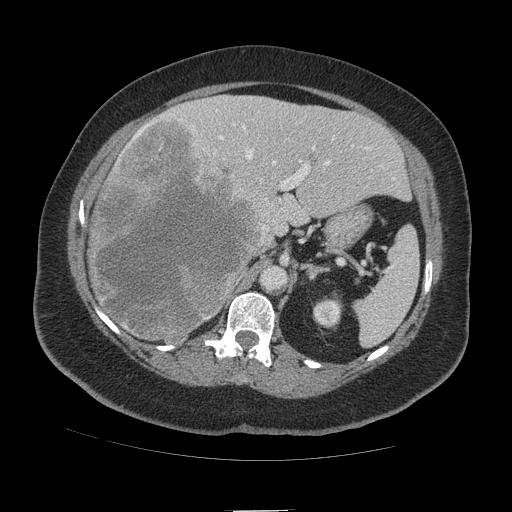
Contrast-enhanced abdominal CT (liver protocol), one axial slice; position 65 of 109 along the scan axis; soft-tissue window (W 400 / L 40 HU); 2.5 mm slice thickness; 512 × 512 image matrix. Case-level facts recorded for this patient, not image findings: diagnosis: hepatocellular carcinoma (patient treated with transarterial chemoembolisation; whether this scan precedes or follows treatment is not stated here); TNM stage (as recorded): Stage-IVB; Child-Pugh class: A; tumour differentiation: poorly differentiated; tumour nodularity: multinodular.
Annotated regions visible in this slice (semi-automatically segmented with operator editing):
- liver parenchyma outside the tumour (the mass and vessels are separate outlines, so this box may not span the whole liver): box from (x=88, y=94) to (x=410, y=336) px
- mass: (x=88, y=117)–(x=262, y=346)
- liver vessels: (x=133, y=109)–(x=395, y=229)